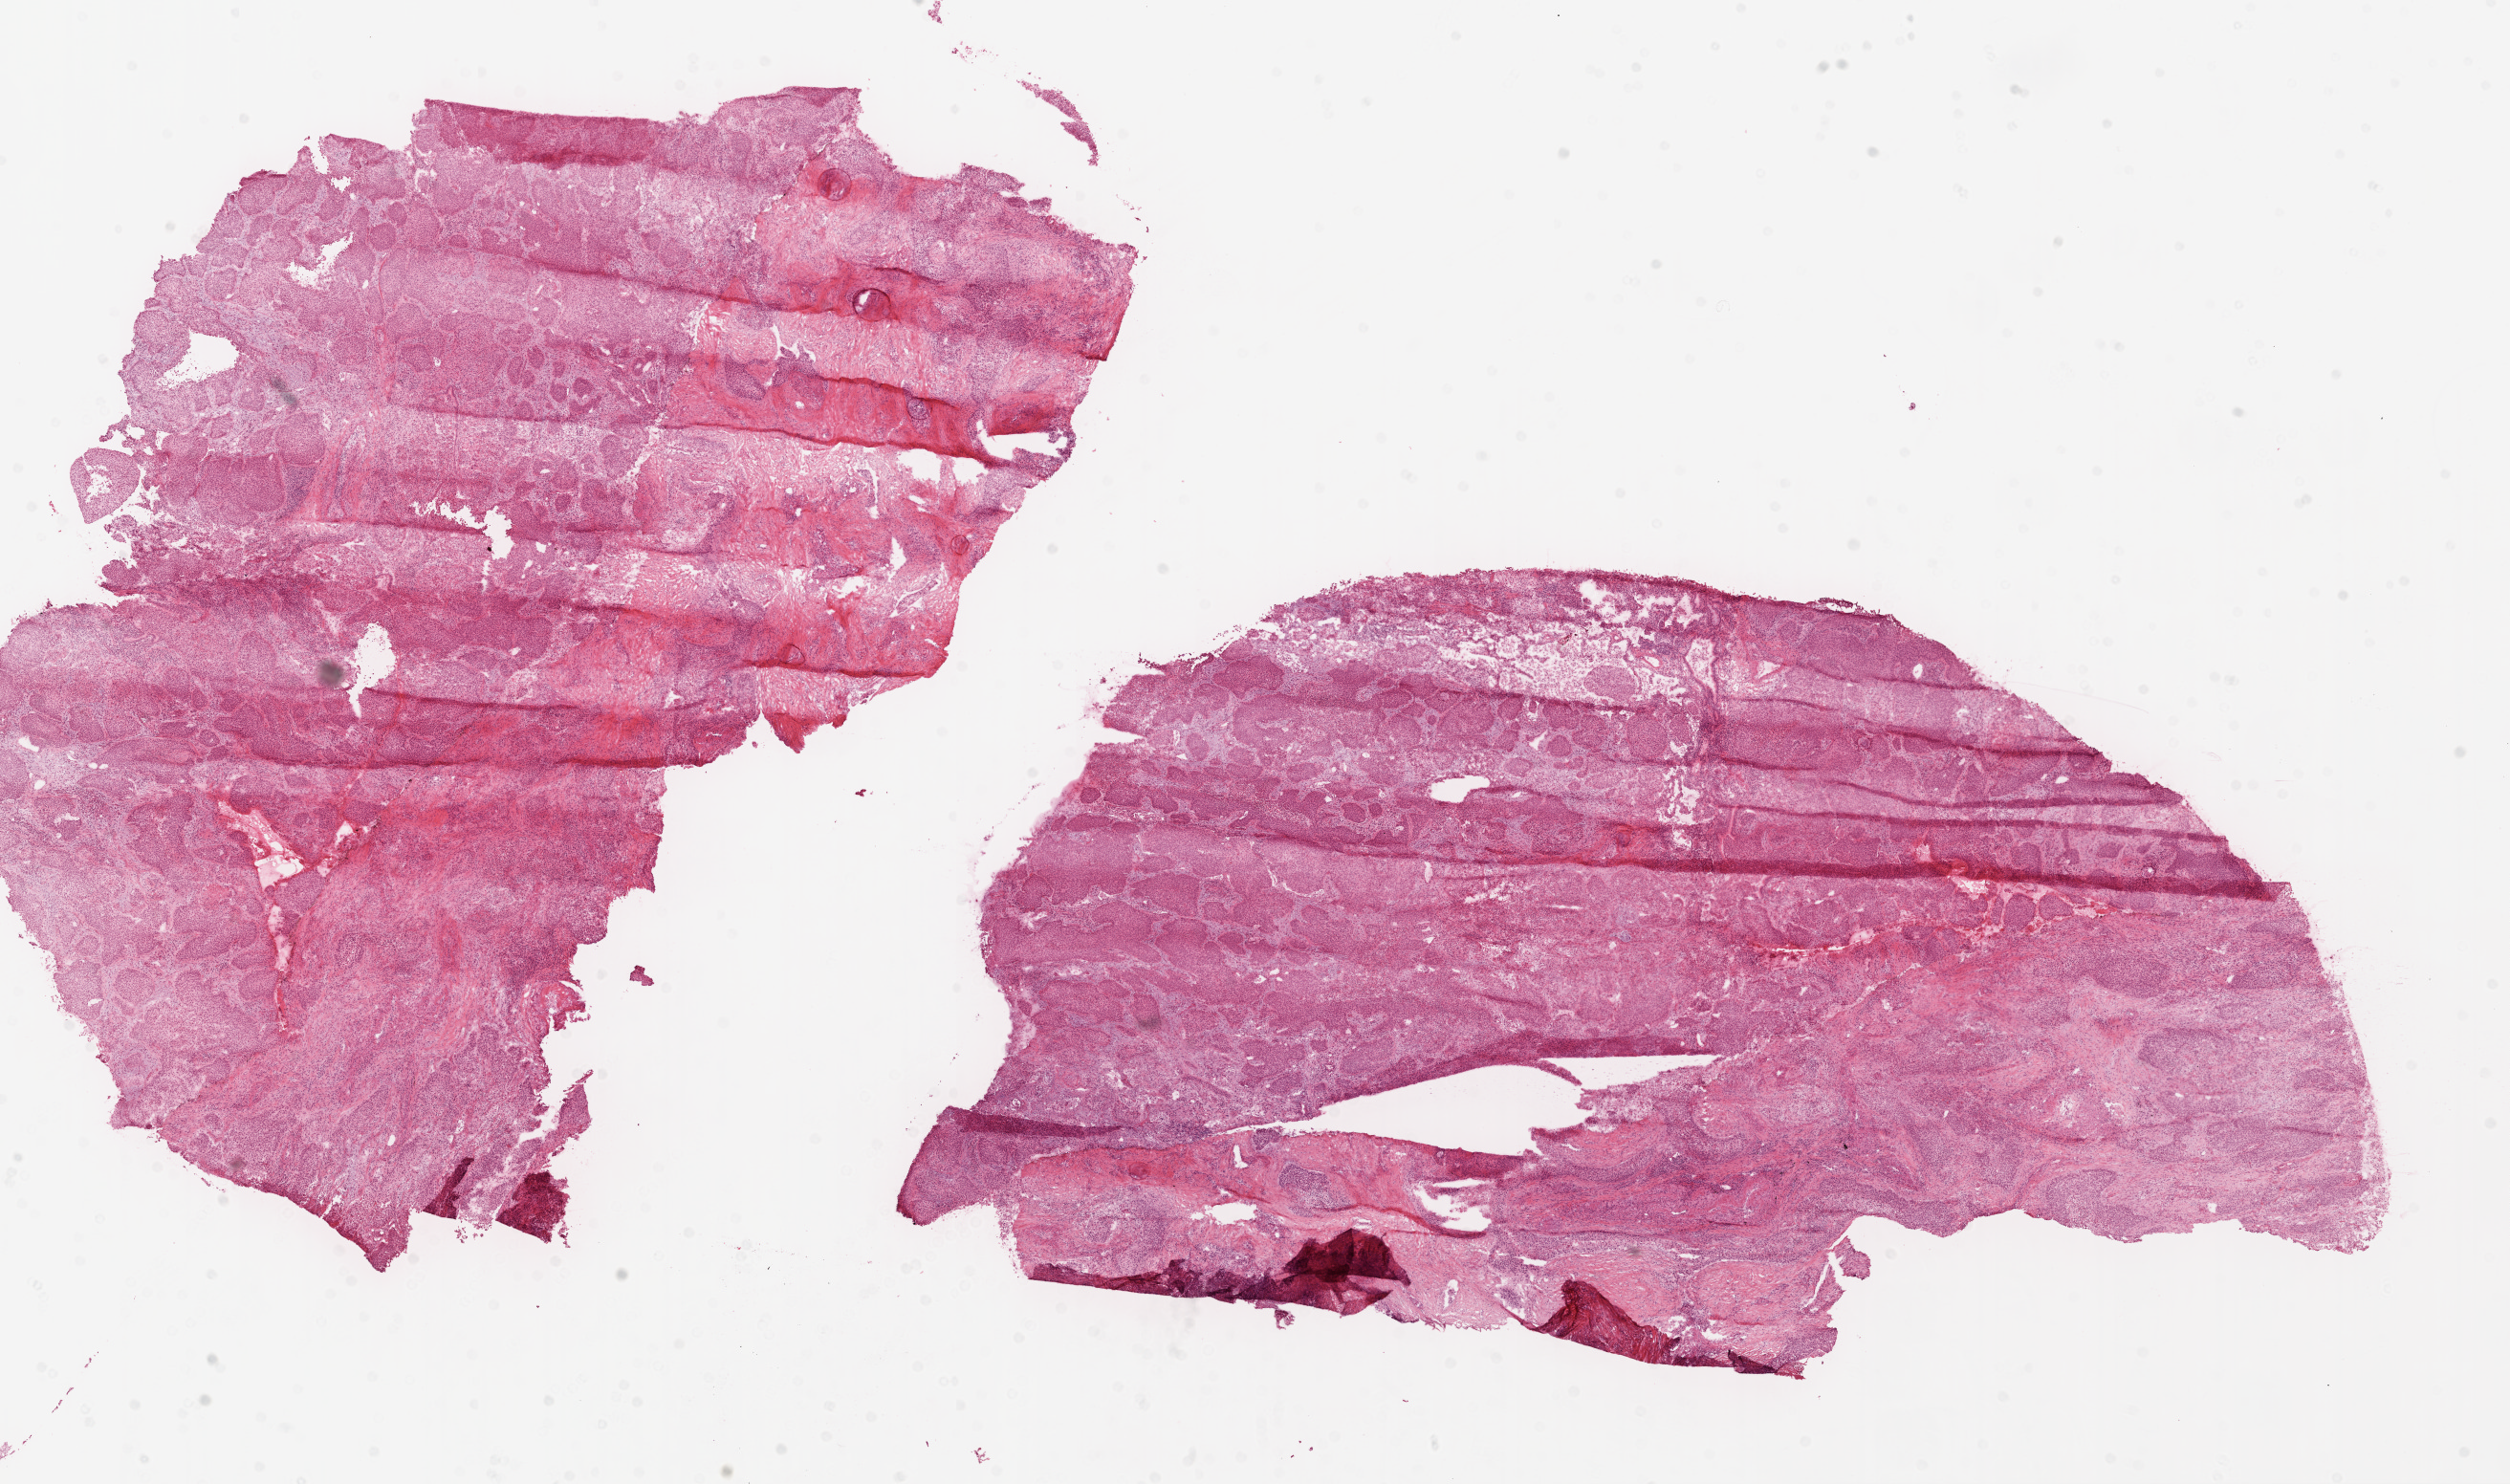
Whole-slide histology image, H&E, a low-resolution overview of the entire scanned area, about 21.1 x 12.5 mm, frozen section, sample: primary tumour, lung. Patient: male, age at initial diagnosis 68 years. Composition of this section per pathologist review: tumour cells 72%, tumour nuclei 80%, normal cells 5%, stromal cells 20%, necrosis 3%.
• AJCC pathologic stage: IB (6th edition)
• diagnosis: Squamous cell carcinoma, NOS (upper lobe, lung)
• laterality: right